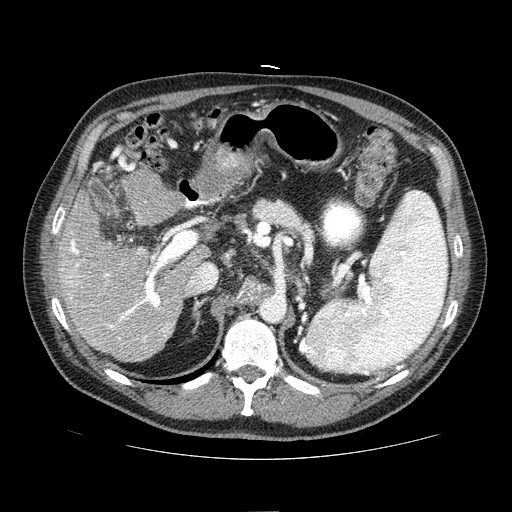
Contrast-enhanced abdominal CT (liver protocol), one axial slice; slice 41 of 81 in the series (ordered by position); one of 2 acquisitions stored at this slice position; soft-tissue window (W 400 / L 40 HU); 2.5 mm slice thickness; 512 × 512 image matrix, field of view 400 × 400 mm. Case-level facts recorded for this patient, not image findings: diagnosis: hepatocellular carcinoma (patient treated with transarterial chemoembolisation; whether this scan precedes or follows treatment is not stated here); TNM stage (as recorded): Stage-IIIA; Child-Pugh class: A; tumour differentiation: well differentiated; tumour nodularity: multinodular.
Structures marked on this image (semi-automatically segmented with operator editing):
- liver parenchyma outside the tumour (the mass and vessels are separate outlines, so this box may not span the whole liver): bounding box (x1, y1, x2, y2) in pixels: (56, 188, 194, 362)
- liver vessels: (60, 231, 169, 342)